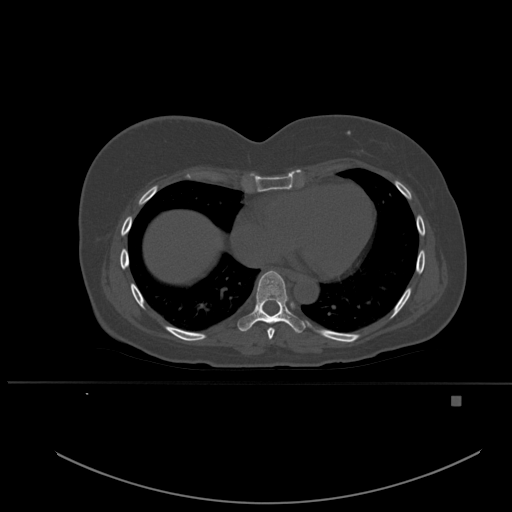
CT including the spine, one axial slice; position 323 of 651 along the scan axis; bone window (W 1800 / L 400 HU); 1.5 mm slice thickness; 512 × 512 image matrix. Female patient, age 49 years. From the clinical record (not read from this slice): primary cancer: breast; vertebrae with lytic lesions (as recorded): L3, T12, L4.
Annotated regions visible in this slice (semi-automatically segmented with operator editing):
- T7 vertebra: bounding box <267,328,275,340> (left, top, right, bottom; pixels)
- T8 vertebra: <238,270,306,333>